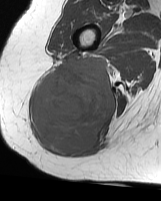
MRI of an extremity soft-tissue mass, one axial slice; position 33 of 70 along the scan axis; MR volume resampled by the dataset authors to the PET/CT grid (not the native acquisition matrix); 3.27 mm slice thickness; 161 × 201 image matrix, field of view 157 × 196 mm. Female patient. From the clinical record (not read from this slice): histological type: synovial sarcoma; grade: intermediate; site of the primary tumour: right buttock.
Structures marked on this image (expert contour drawn on MRI and transferred to this co-registered scan by the dataset authors):
- gross tumour volume including surrounding oedema: box from (x=33, y=54) to (x=116, y=155) px
- gross tumour volume (mass): (x=33, y=54)–(x=116, y=155)